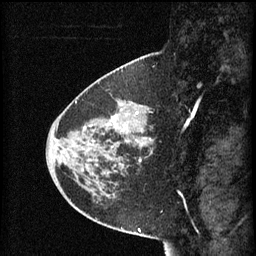
Breast MRI (dynamic contrast-enhanced), one sagittal slice. 3 images stored at this slice position (order not interpretable as contrast timing). 1.5 T. TE 4.2 ms, TR 8.2 ms. 2 mm slice thickness. 256 × 256 image matrix, field of view 200 × 200 mm. Patient: female, 45 years.
Outlined on this slice (semi-automatic segmentation, software-assisted and operator-edited):
- analysis volume of interest (the breast-tissue region the enhancement analysis was run in; not a lesion): bounding box (x1, y1, x2, y2) in pixels: (80, 102, 152, 171)
- tumour enhancement mask (voxels above the 70 % enhancement threshold inside the analysis volume of interest): (113, 116, 141, 163)